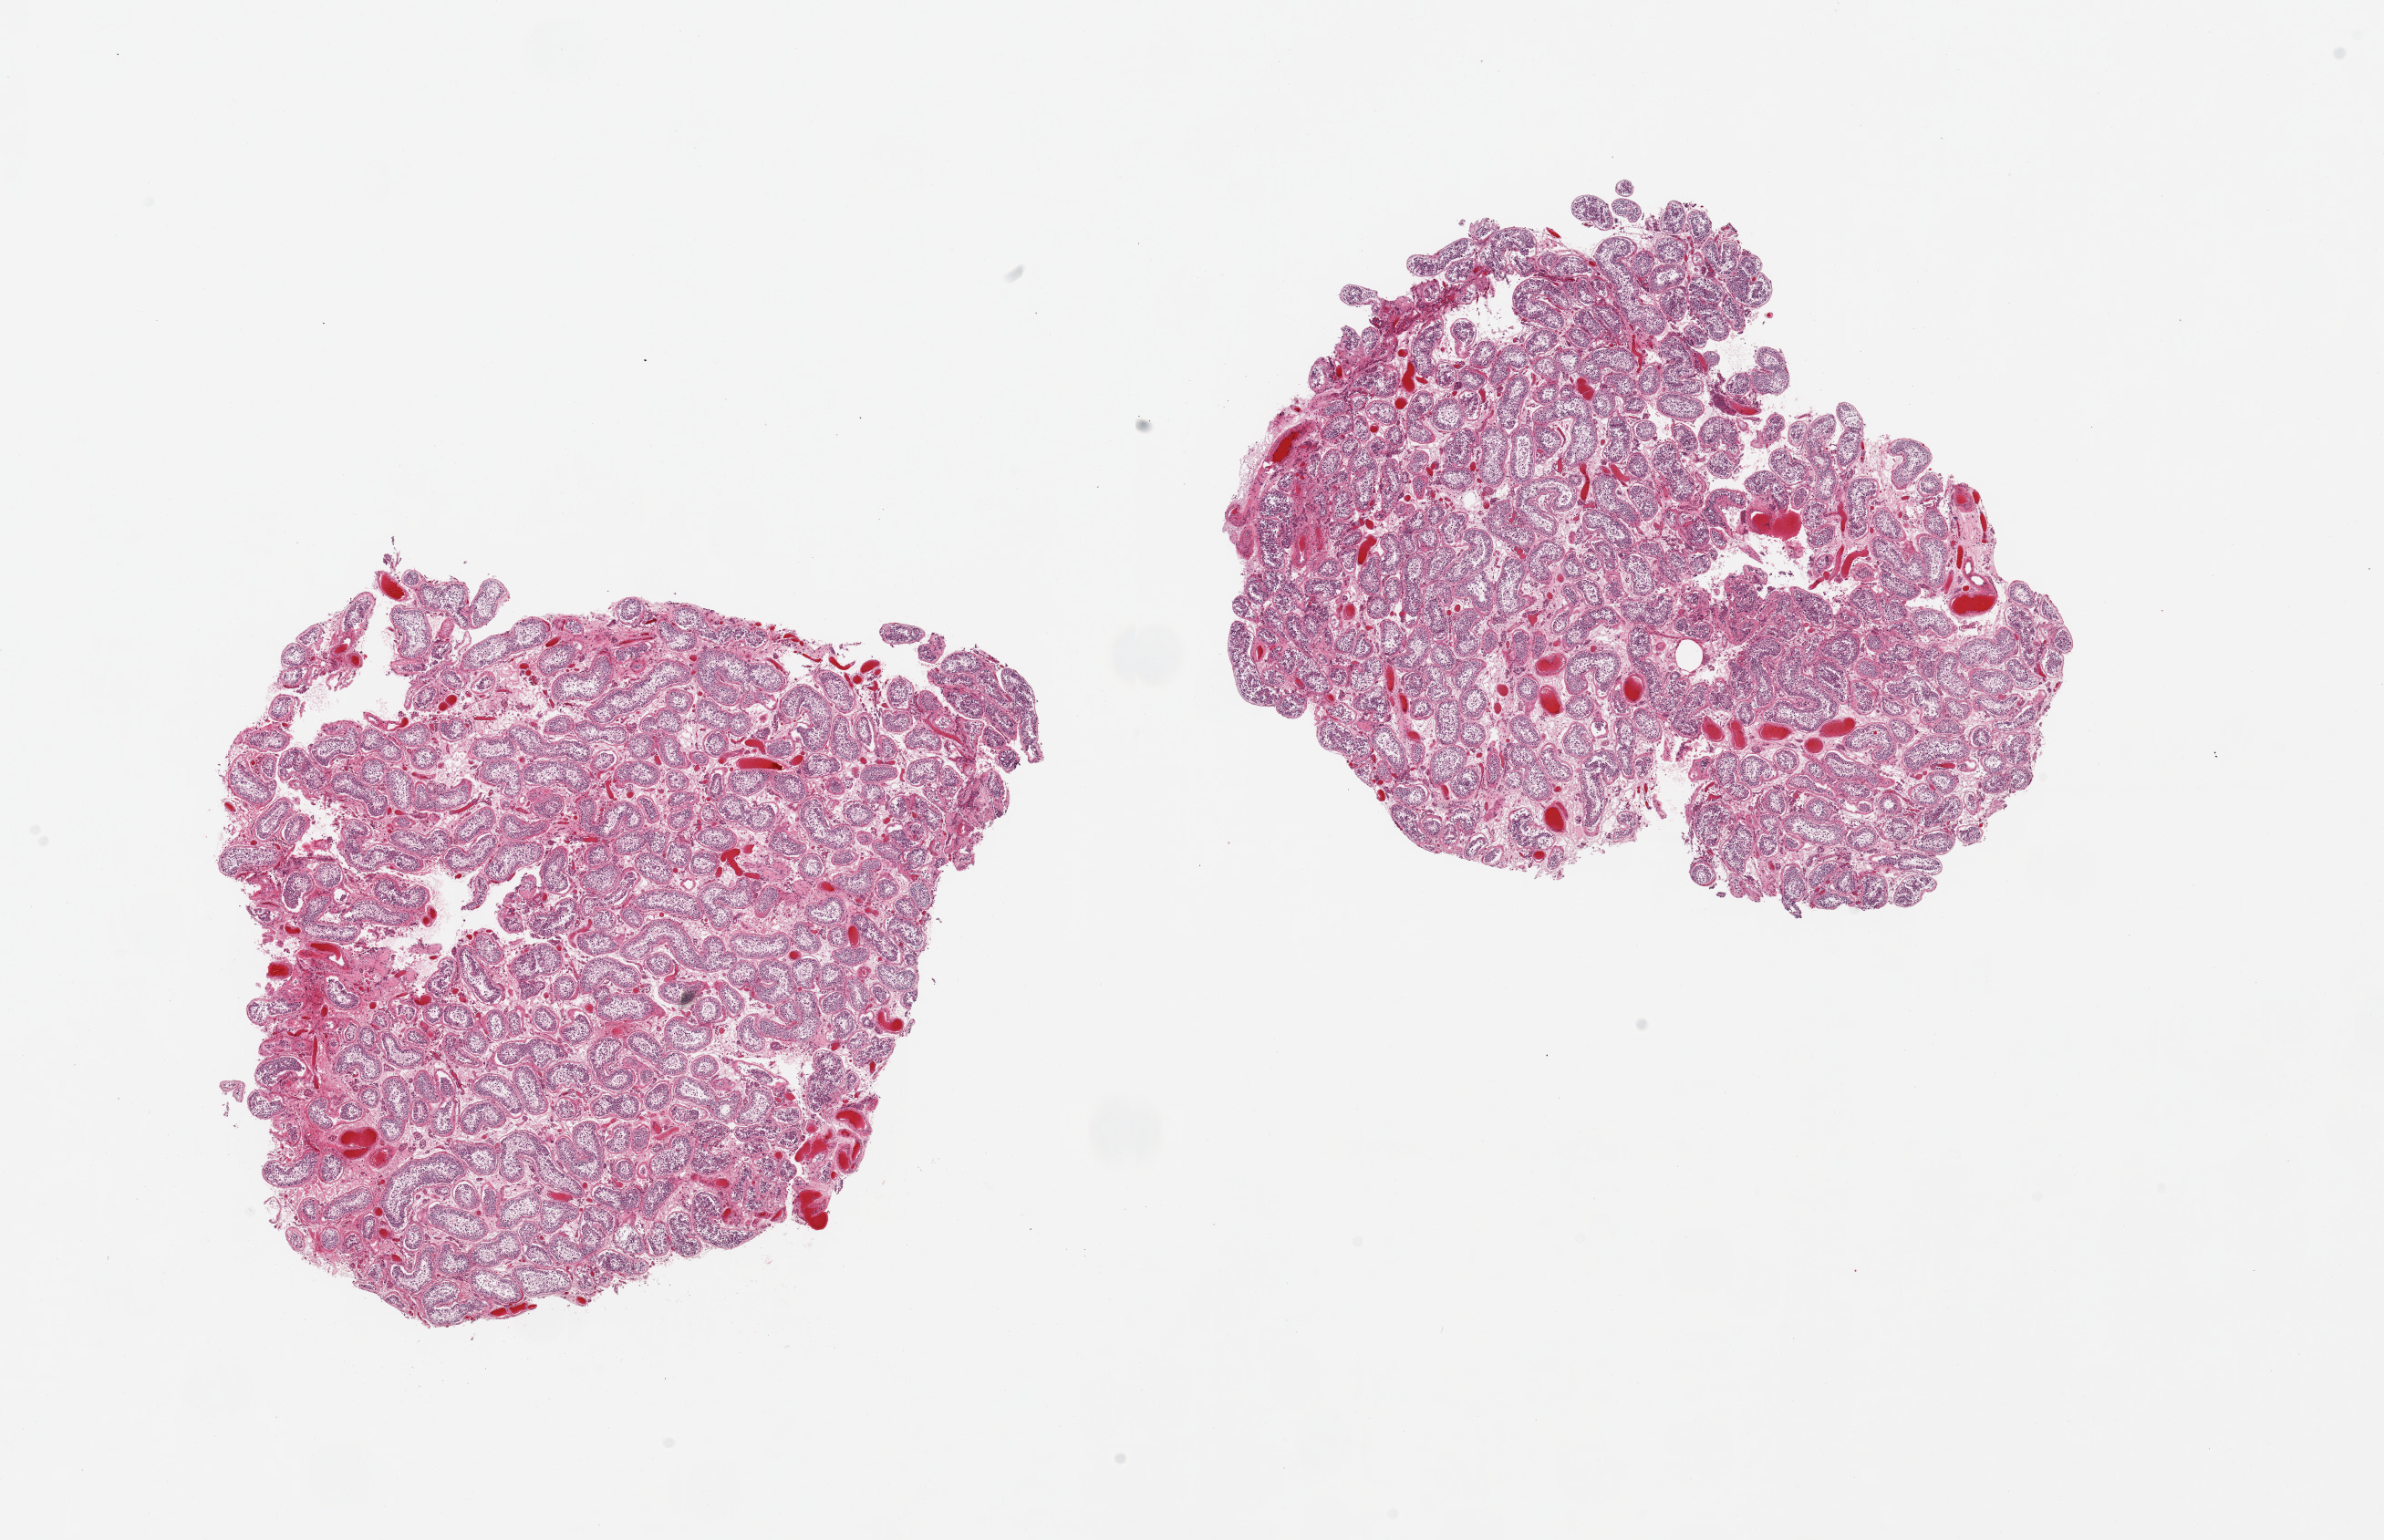
Whole-slide image, hematoxylin and eosin (H&E) stain, brightfield — a low-resolution overview of the entire scanned area, about 20.7 x 13.4 mm (slide scanned at 20x); PAXgene-fixed paraffin-embedded (PFPE) section; section of testis (target tissue); donor tissue sample. Donor sex: male.
• reviewer comment on this tissue sample: 2 pieces; spermatogenesis present; congestion